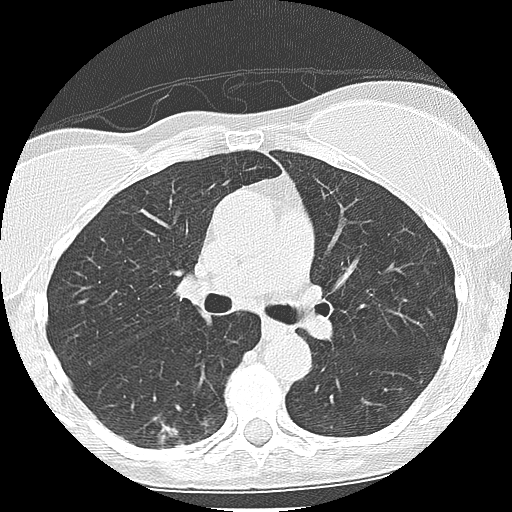
Low-dose screening chest CT, one axial slice. Position 128 of 225 along the scan axis. Reconstruction kernel LUNG. 120 kVp. Lung window (W 1500 / L -600 HU). 2.5 mm slice thickness. 512 × 512 image matrix.
Structures marked on this image (manually delineated by an expert):
- lesion 1 (tumor, lower lobe of right lung): bounding box [x1, y1, x2, y2] px = [158, 425, 184, 449]